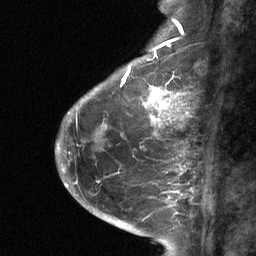
Breast MRI (dynamic contrast-enhanced), one sagittal slice; slice 21 of 64 in the series (ordered by position); dynamic contrast-enhanced study with each time point stored as its own series, time point 2 of 3 at this slice position (early post-contrast, ordered by acquisition time); 1.5 T; TE 4.8 ms, TR 27 ms; 2 mm slice thickness; 256 × 256 image matrix, field of view 180 × 180 mm. Patient: female, 59 years. Case-level facts recorded for this patient, not image findings: setting: breast cancer imaged before/during neoadjuvant chemotherapy; receptor status: triple-negative.
Structures marked on this image (semi-automatic segmentation, software-assisted and operator-edited):
- analysis volume of interest (the breast-tissue region the enhancement analysis was run in; not a lesion): box from (x=113, y=82) to (x=175, y=120) px
- tumour enhancement mask (voxels above the 90 % enhancement threshold inside the analysis volume of interest): (x=143, y=87)–(x=171, y=120)